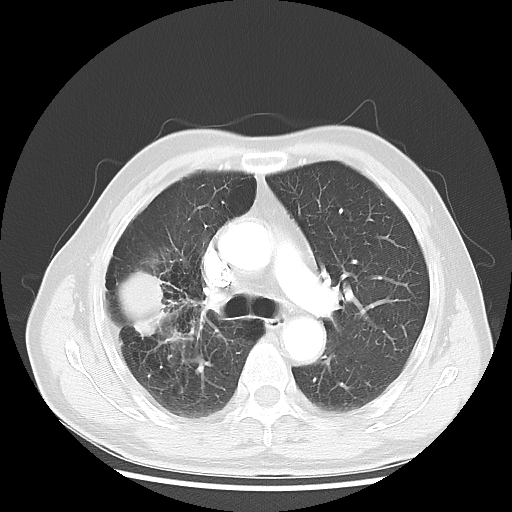
Chest CT, one axial slice; slice 31 of 50 in the series (ordered by position); lung window (W 1500 / L -600 HU); 512 × 512 image matrix. Patient: male, 69 years. From the clinical record (not read from this slice): clinical TNM (as recorded): T3 N0 M0; histopathological grade: G3.
Annotated regions visible in this slice (bounding box drawn by a radiologist):
- lung tumour (recorded histology: adenocarcinoma): bounding box <119,269,174,338> (left, top, right, bottom; pixels)